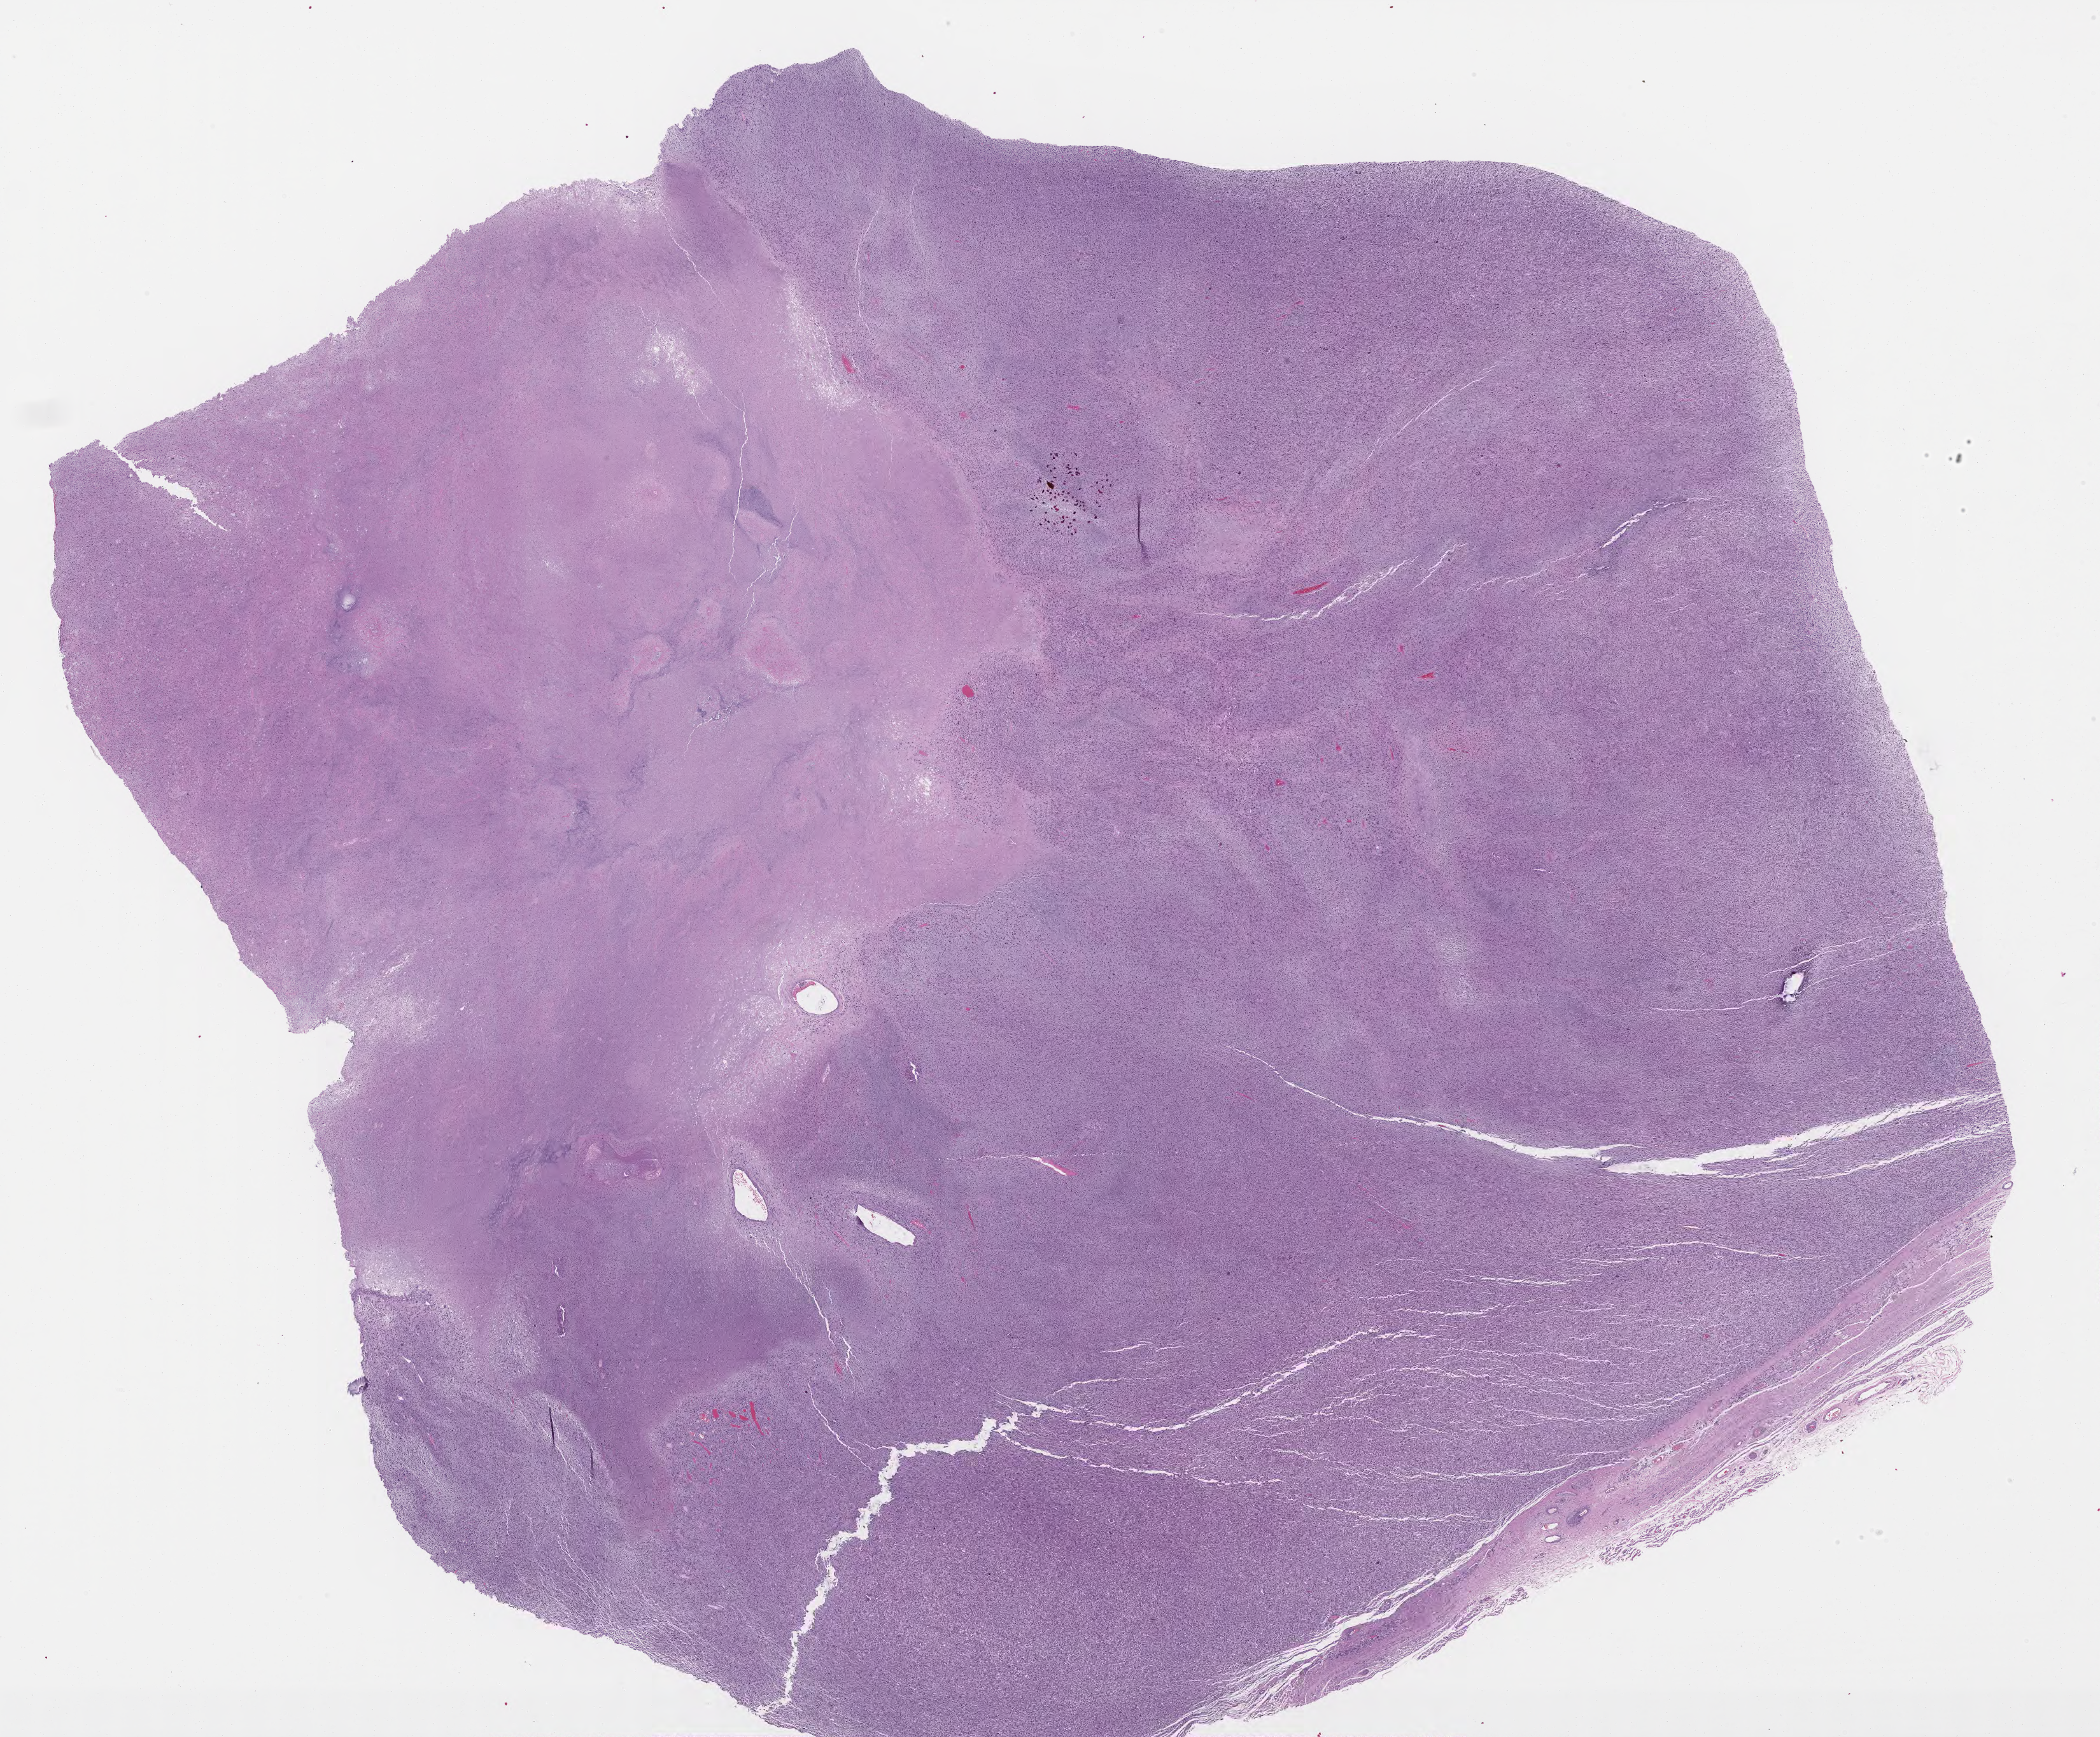
Hematoxylin and eosin (H&E) stained whole-slide image, low-resolution overview of the scanned area, about 26.5 x 21.9 mm (slide scanned at 40x); FFPE section; primary tumour sample from the connective, subcutaneous and other soft tissues. Female patient; age at initial diagnosis 78 years.
• pathologic diagnosis: Undifferentiated sarcoma (connective, subcutaneous and other soft tissues of lower limb and hip)